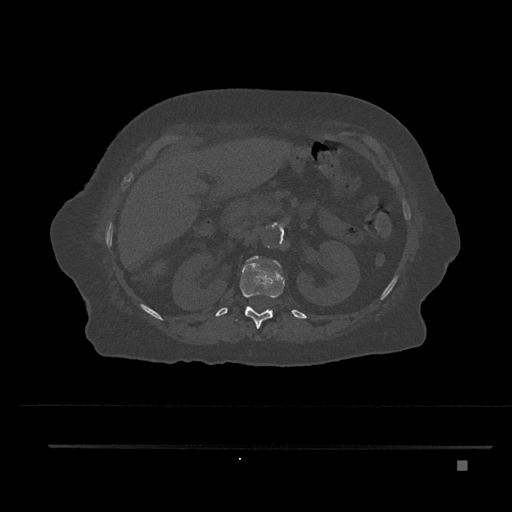
CT including the spine, one axial slice; slice 254 of 797 in the series (ordered by position); reconstruction kernel Br40s/3; 120 kVp; bone window (W 1800 / L 400 HU); 0.5 mm slice thickness; 512 × 512 image matrix, field of view 437 × 437 mm. Patient: female, 76 years. From the clinical record (not read from this slice): primary cancer: lung; vertebrae with lytic lesions (as recorded): T11, L3.
Outlined on this slice (semi-automatically segmented with operator editing):
- L1 vertebra: box from (x=242, y=256) to (x=282, y=274) px
- T12 vertebra: (x=235, y=262)–(x=285, y=329)